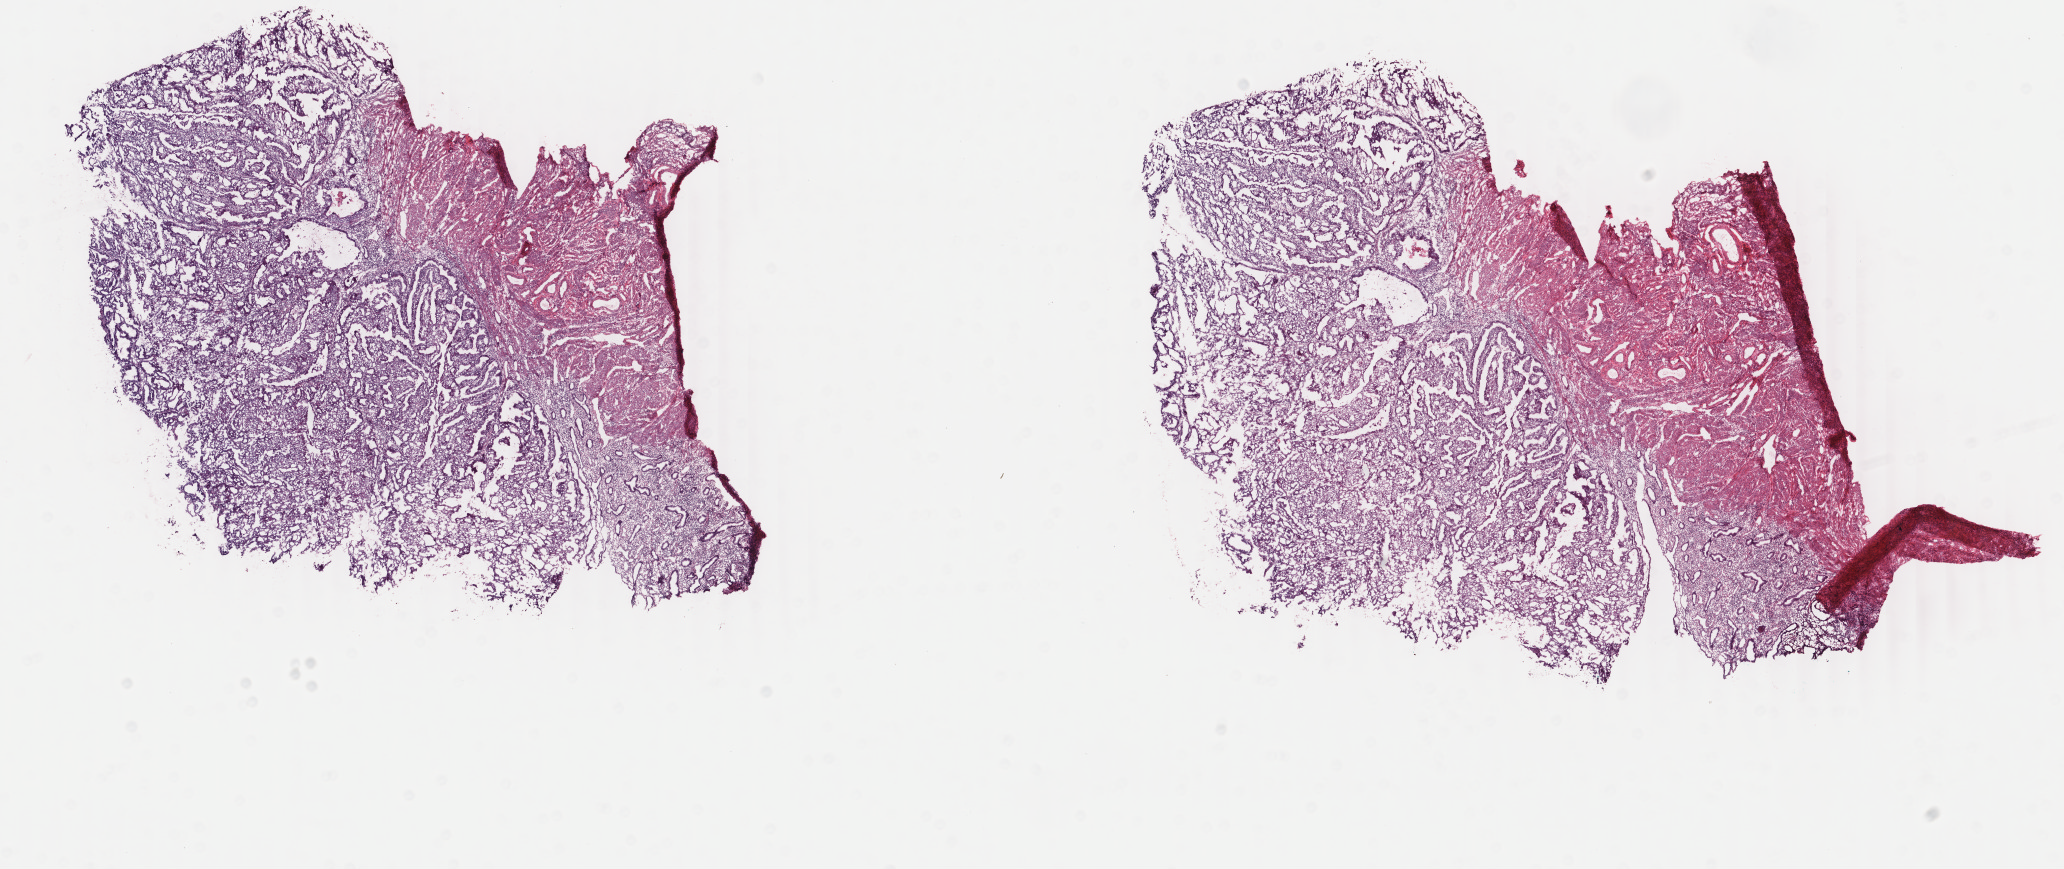
Whole-slide histology image, H&E, a low-resolution overview of the entire scanned area, about 16.4 x 6.9 mm. Frozen section. Uterus, primary tumour sample. Female patient; age at initial diagnosis 54 years. Histologic grade: G1 (well differentiated). Slide review estimates, as recorded: tumour cells 75%, tumour nuclei 70%, normal cells 0%, stromal cells 25%, necrosis 0%. Inflammatory infiltration, as recorded: lymphocyte infiltration 0%, monocyte infiltration 0%, neutrophil infiltration 0%.
* histologic diagnosis: Endometrioid adenocarcinoma, NOS (endometrium)
* FIGO stage: IA